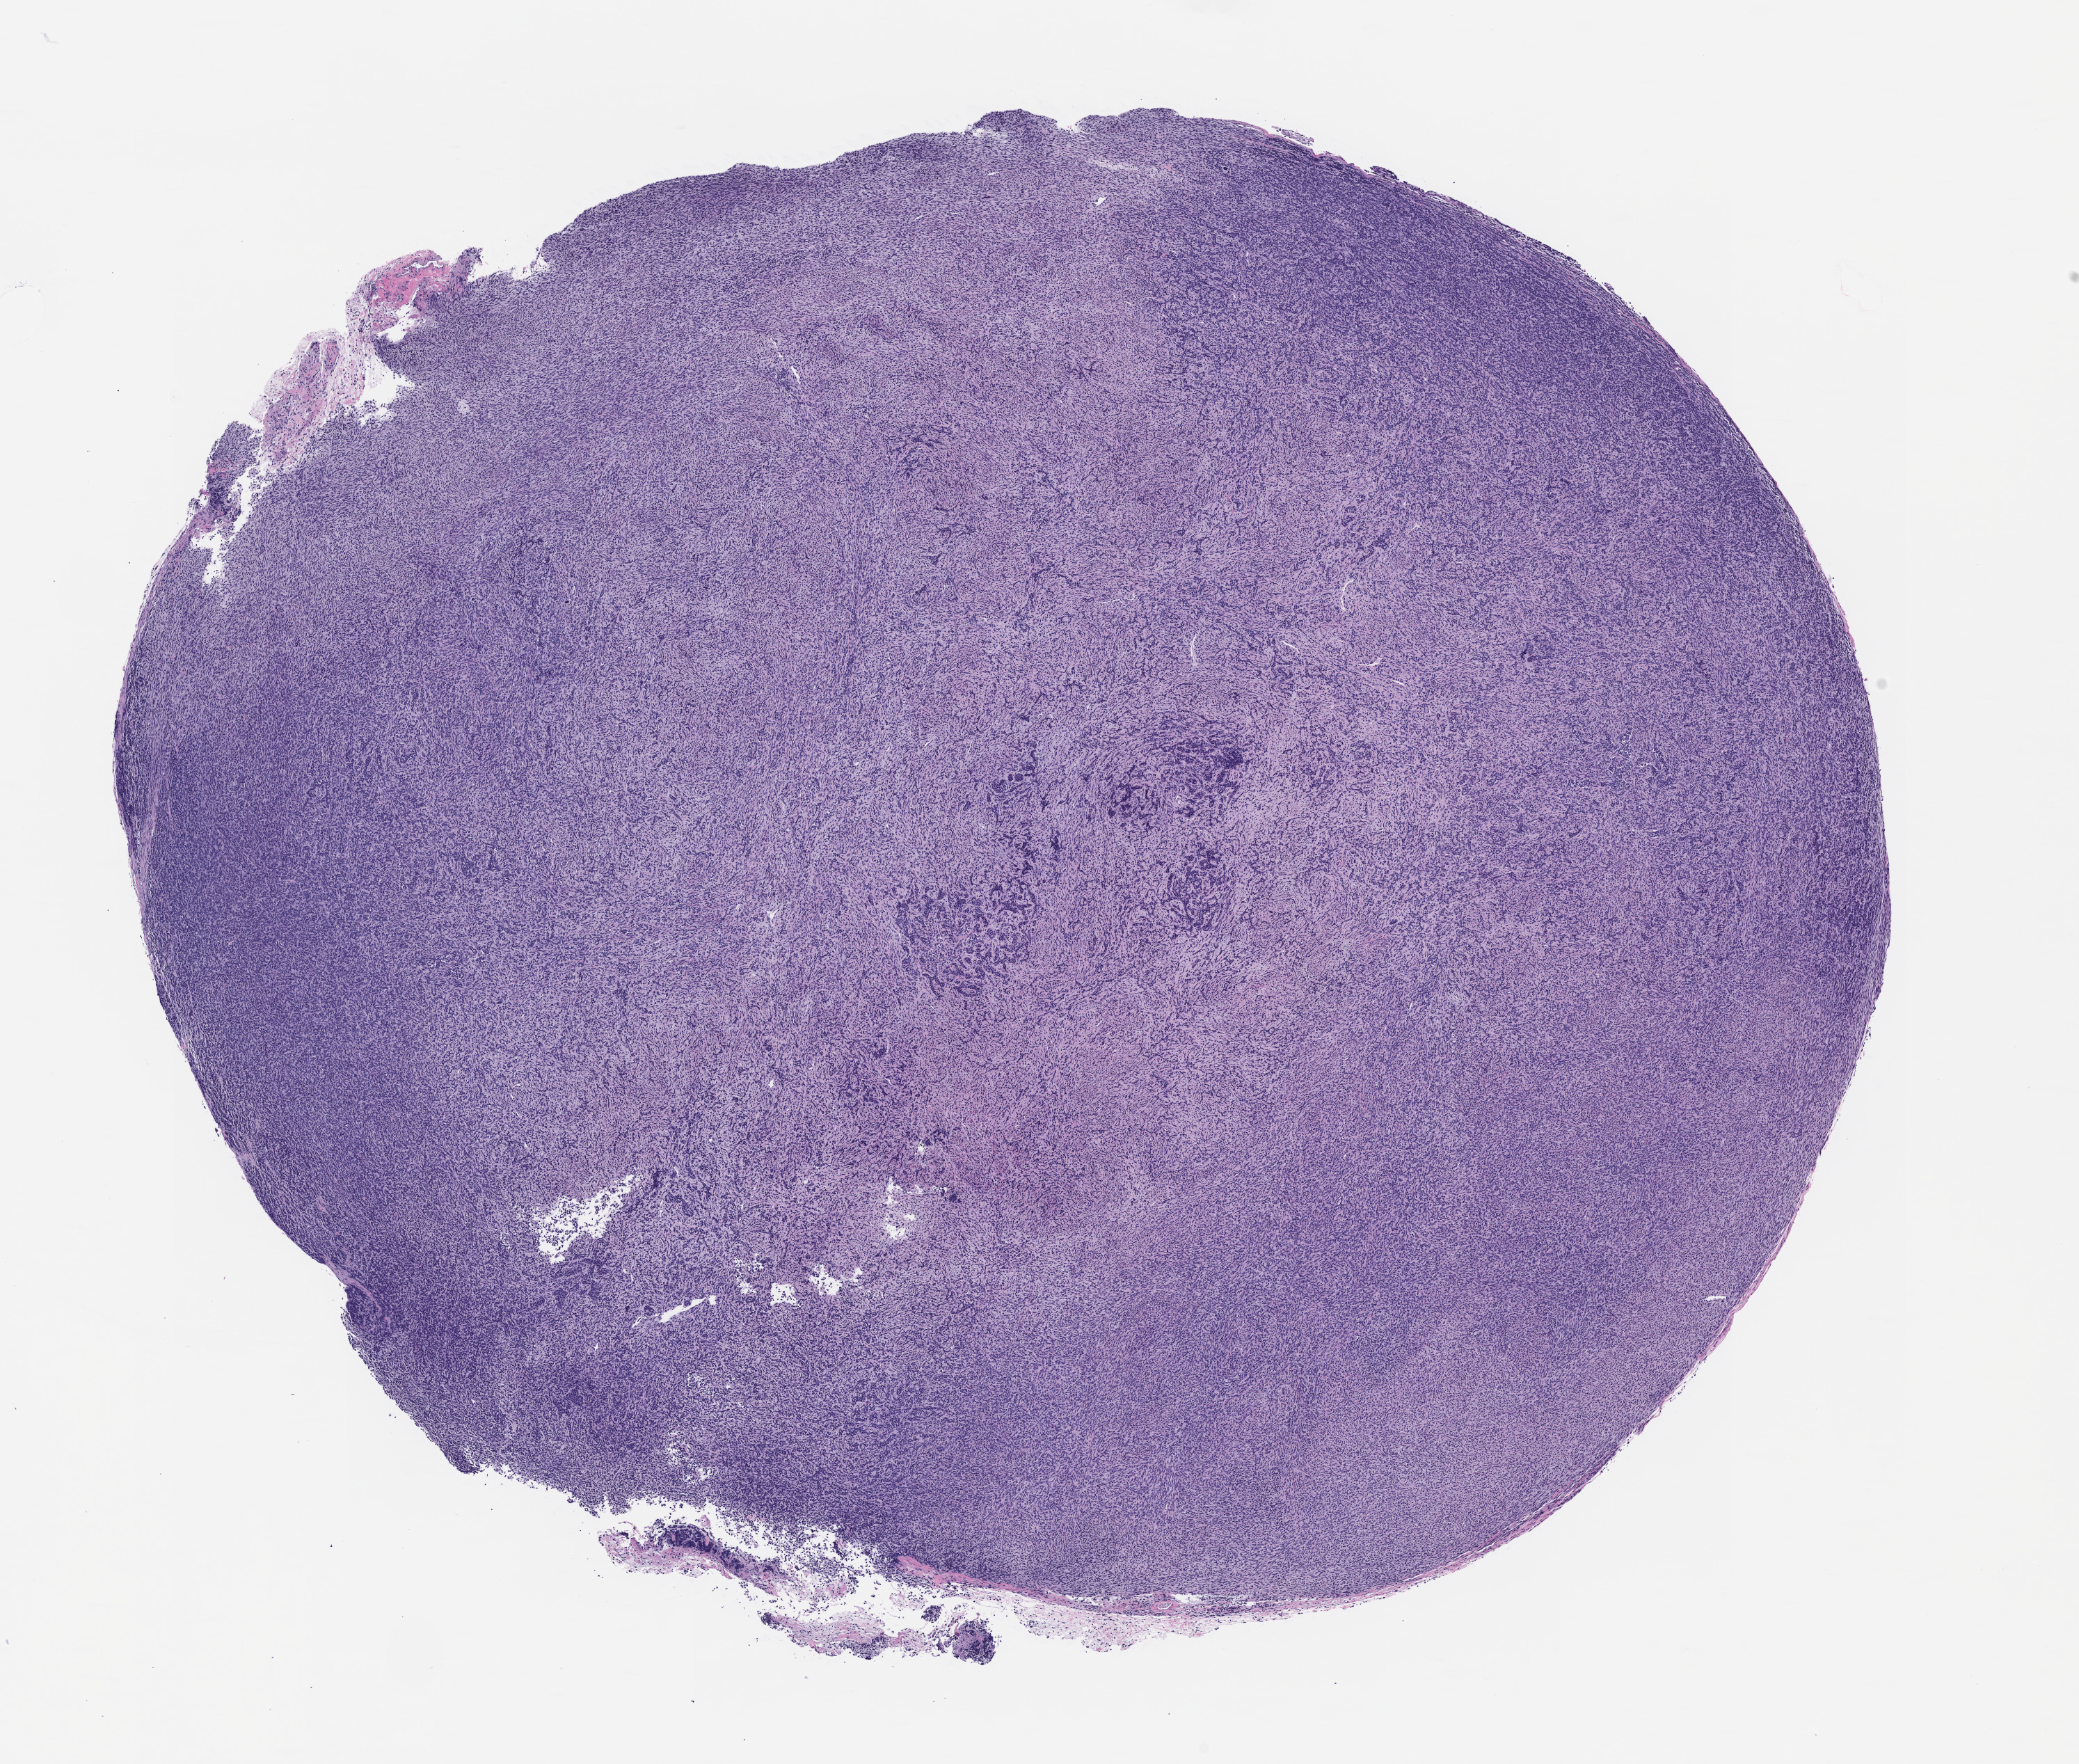
Haematoxylin and eosin whole-slide image of a patient-derived xenograft (PDX) tumor grown in a mouse, passage 1, shown as a low-resolution overview of the whole scanned area (about 12.0 x 10.2 mm), formalin-fixed, paraffin-embedded (FFPE) tissue, tumor site category: peripheral nervous system.
• originating patient diagnosis: Malignant Peripheral Nerve Sheath Tumor